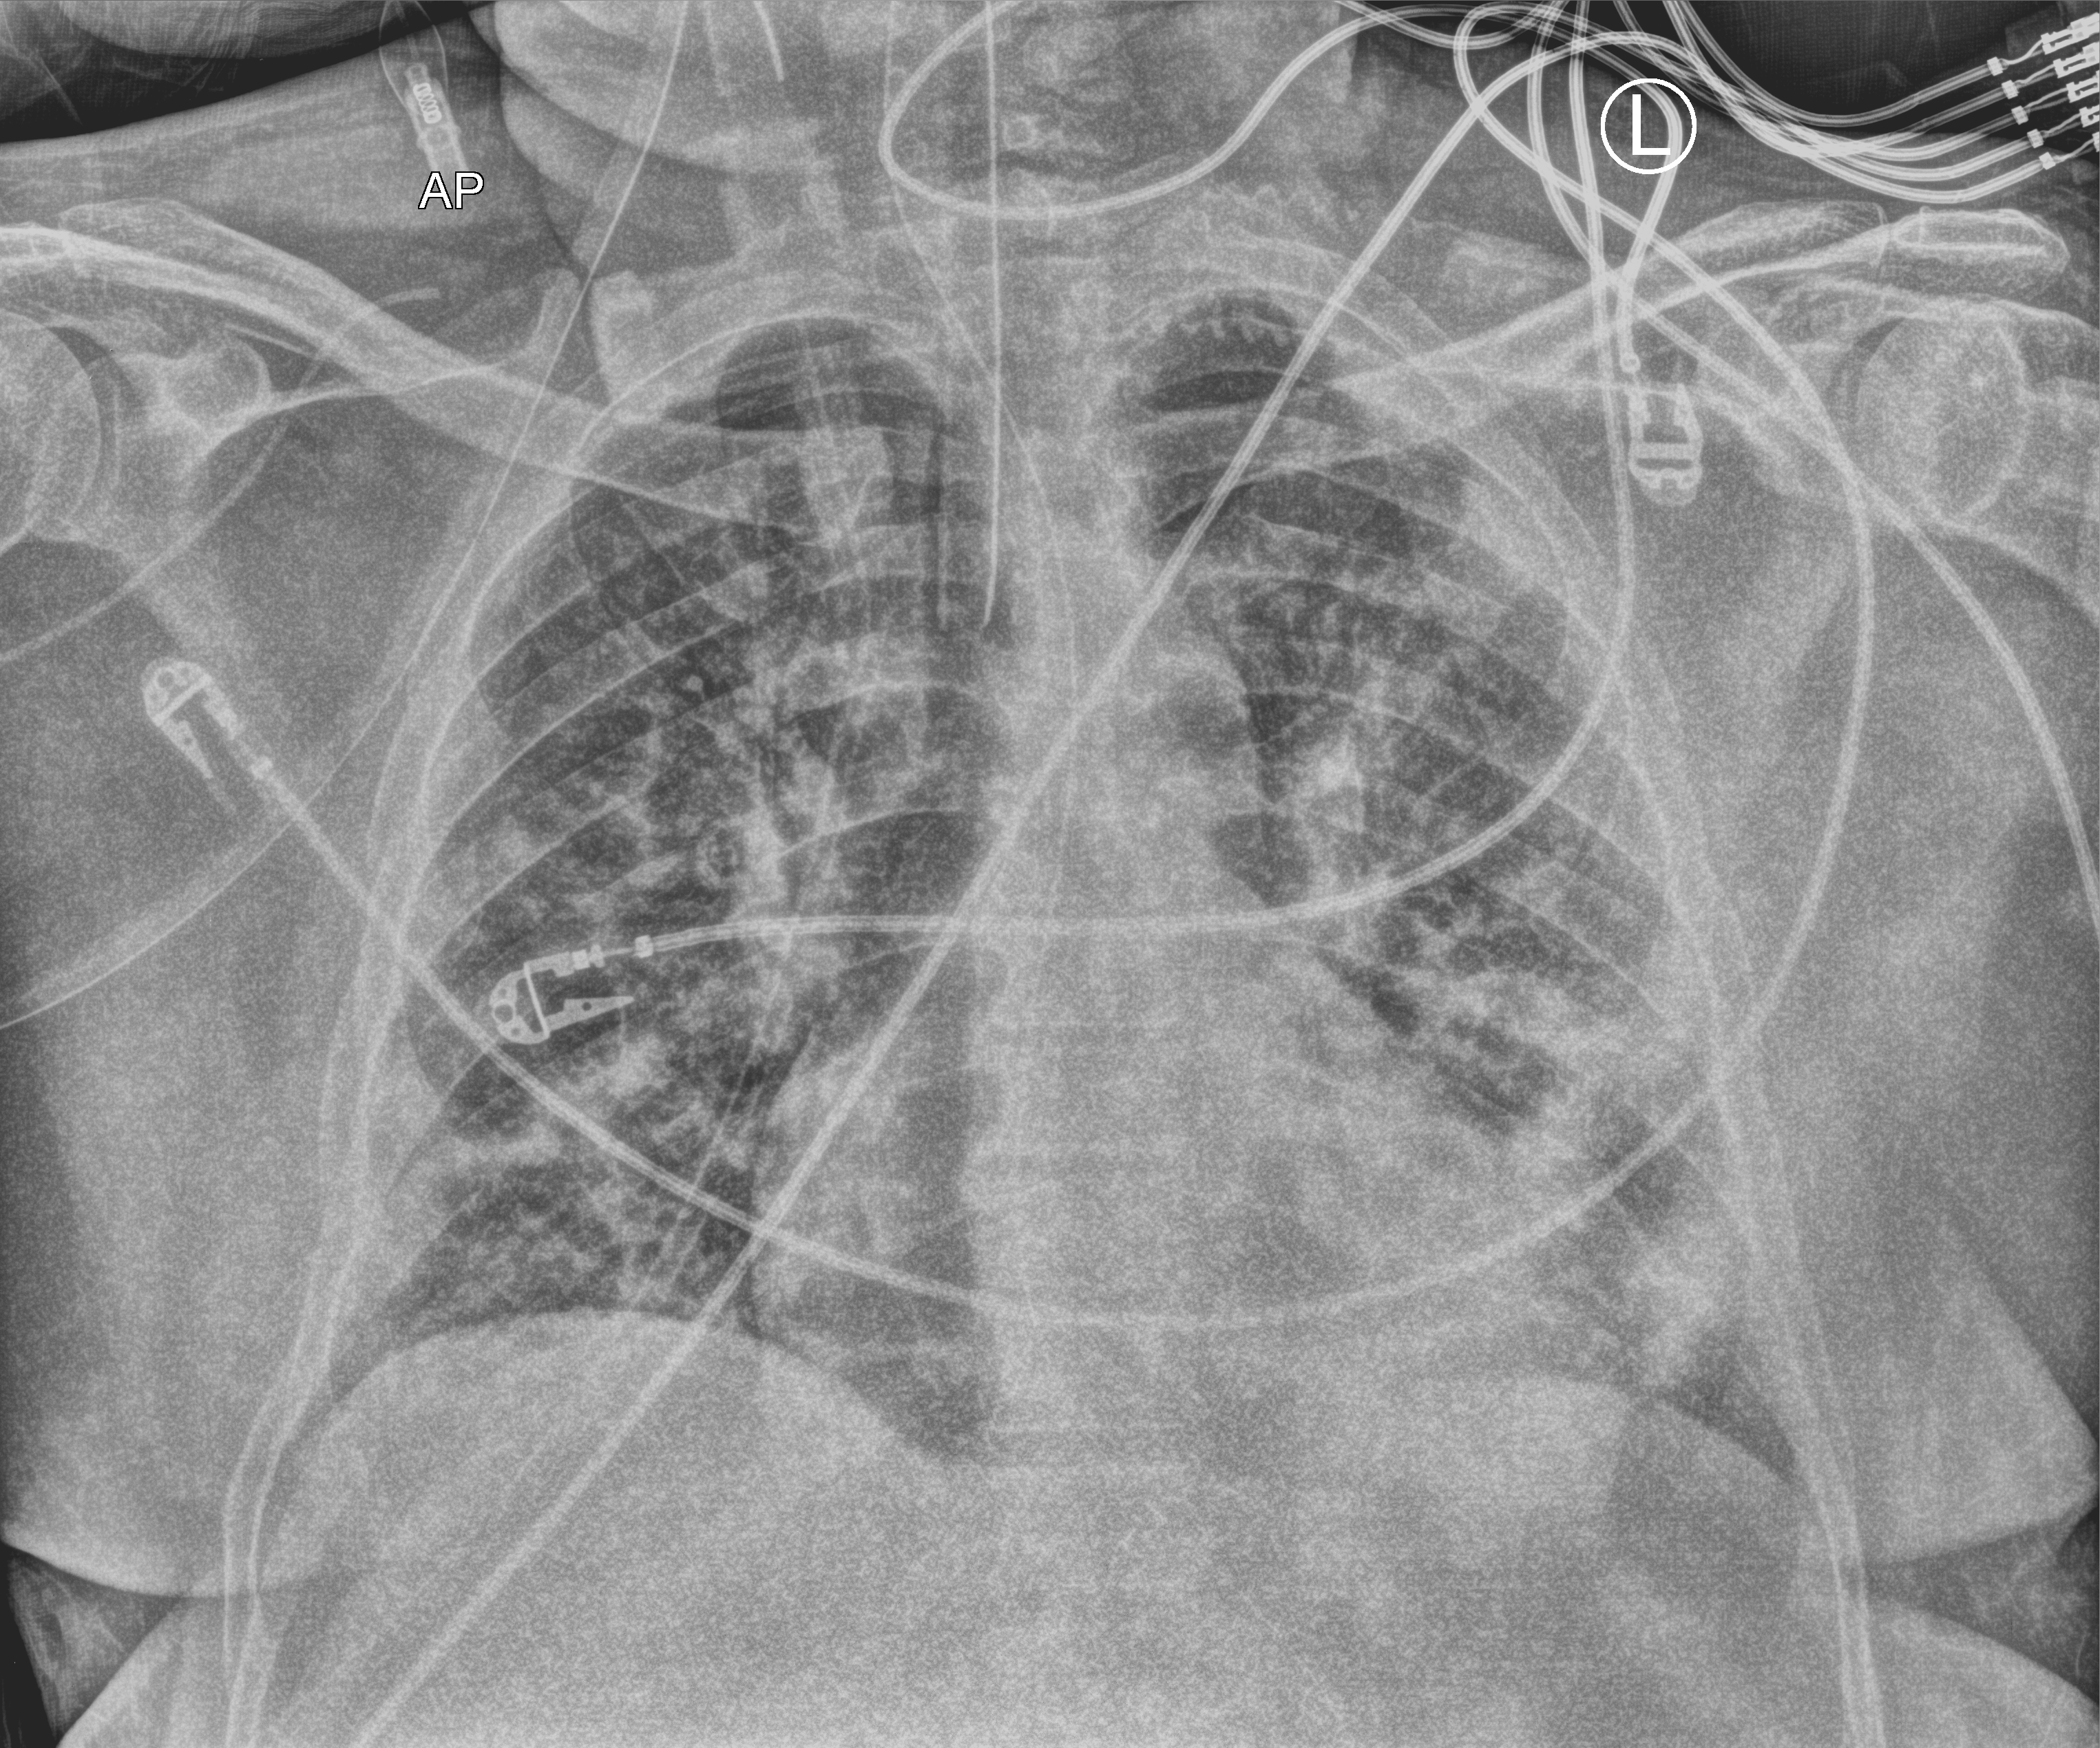
Bedside chest radiograph (computed radiography), anteroposterior (AP) projection. Patient hospitalised with COVID-19; male, aged 18–59 years.
Hospital-stay facts (about this admission, not read from this image; timing relative to this image not recorded): mechanically ventilated during this hospital stay: yes; hypertension (admission record): no.